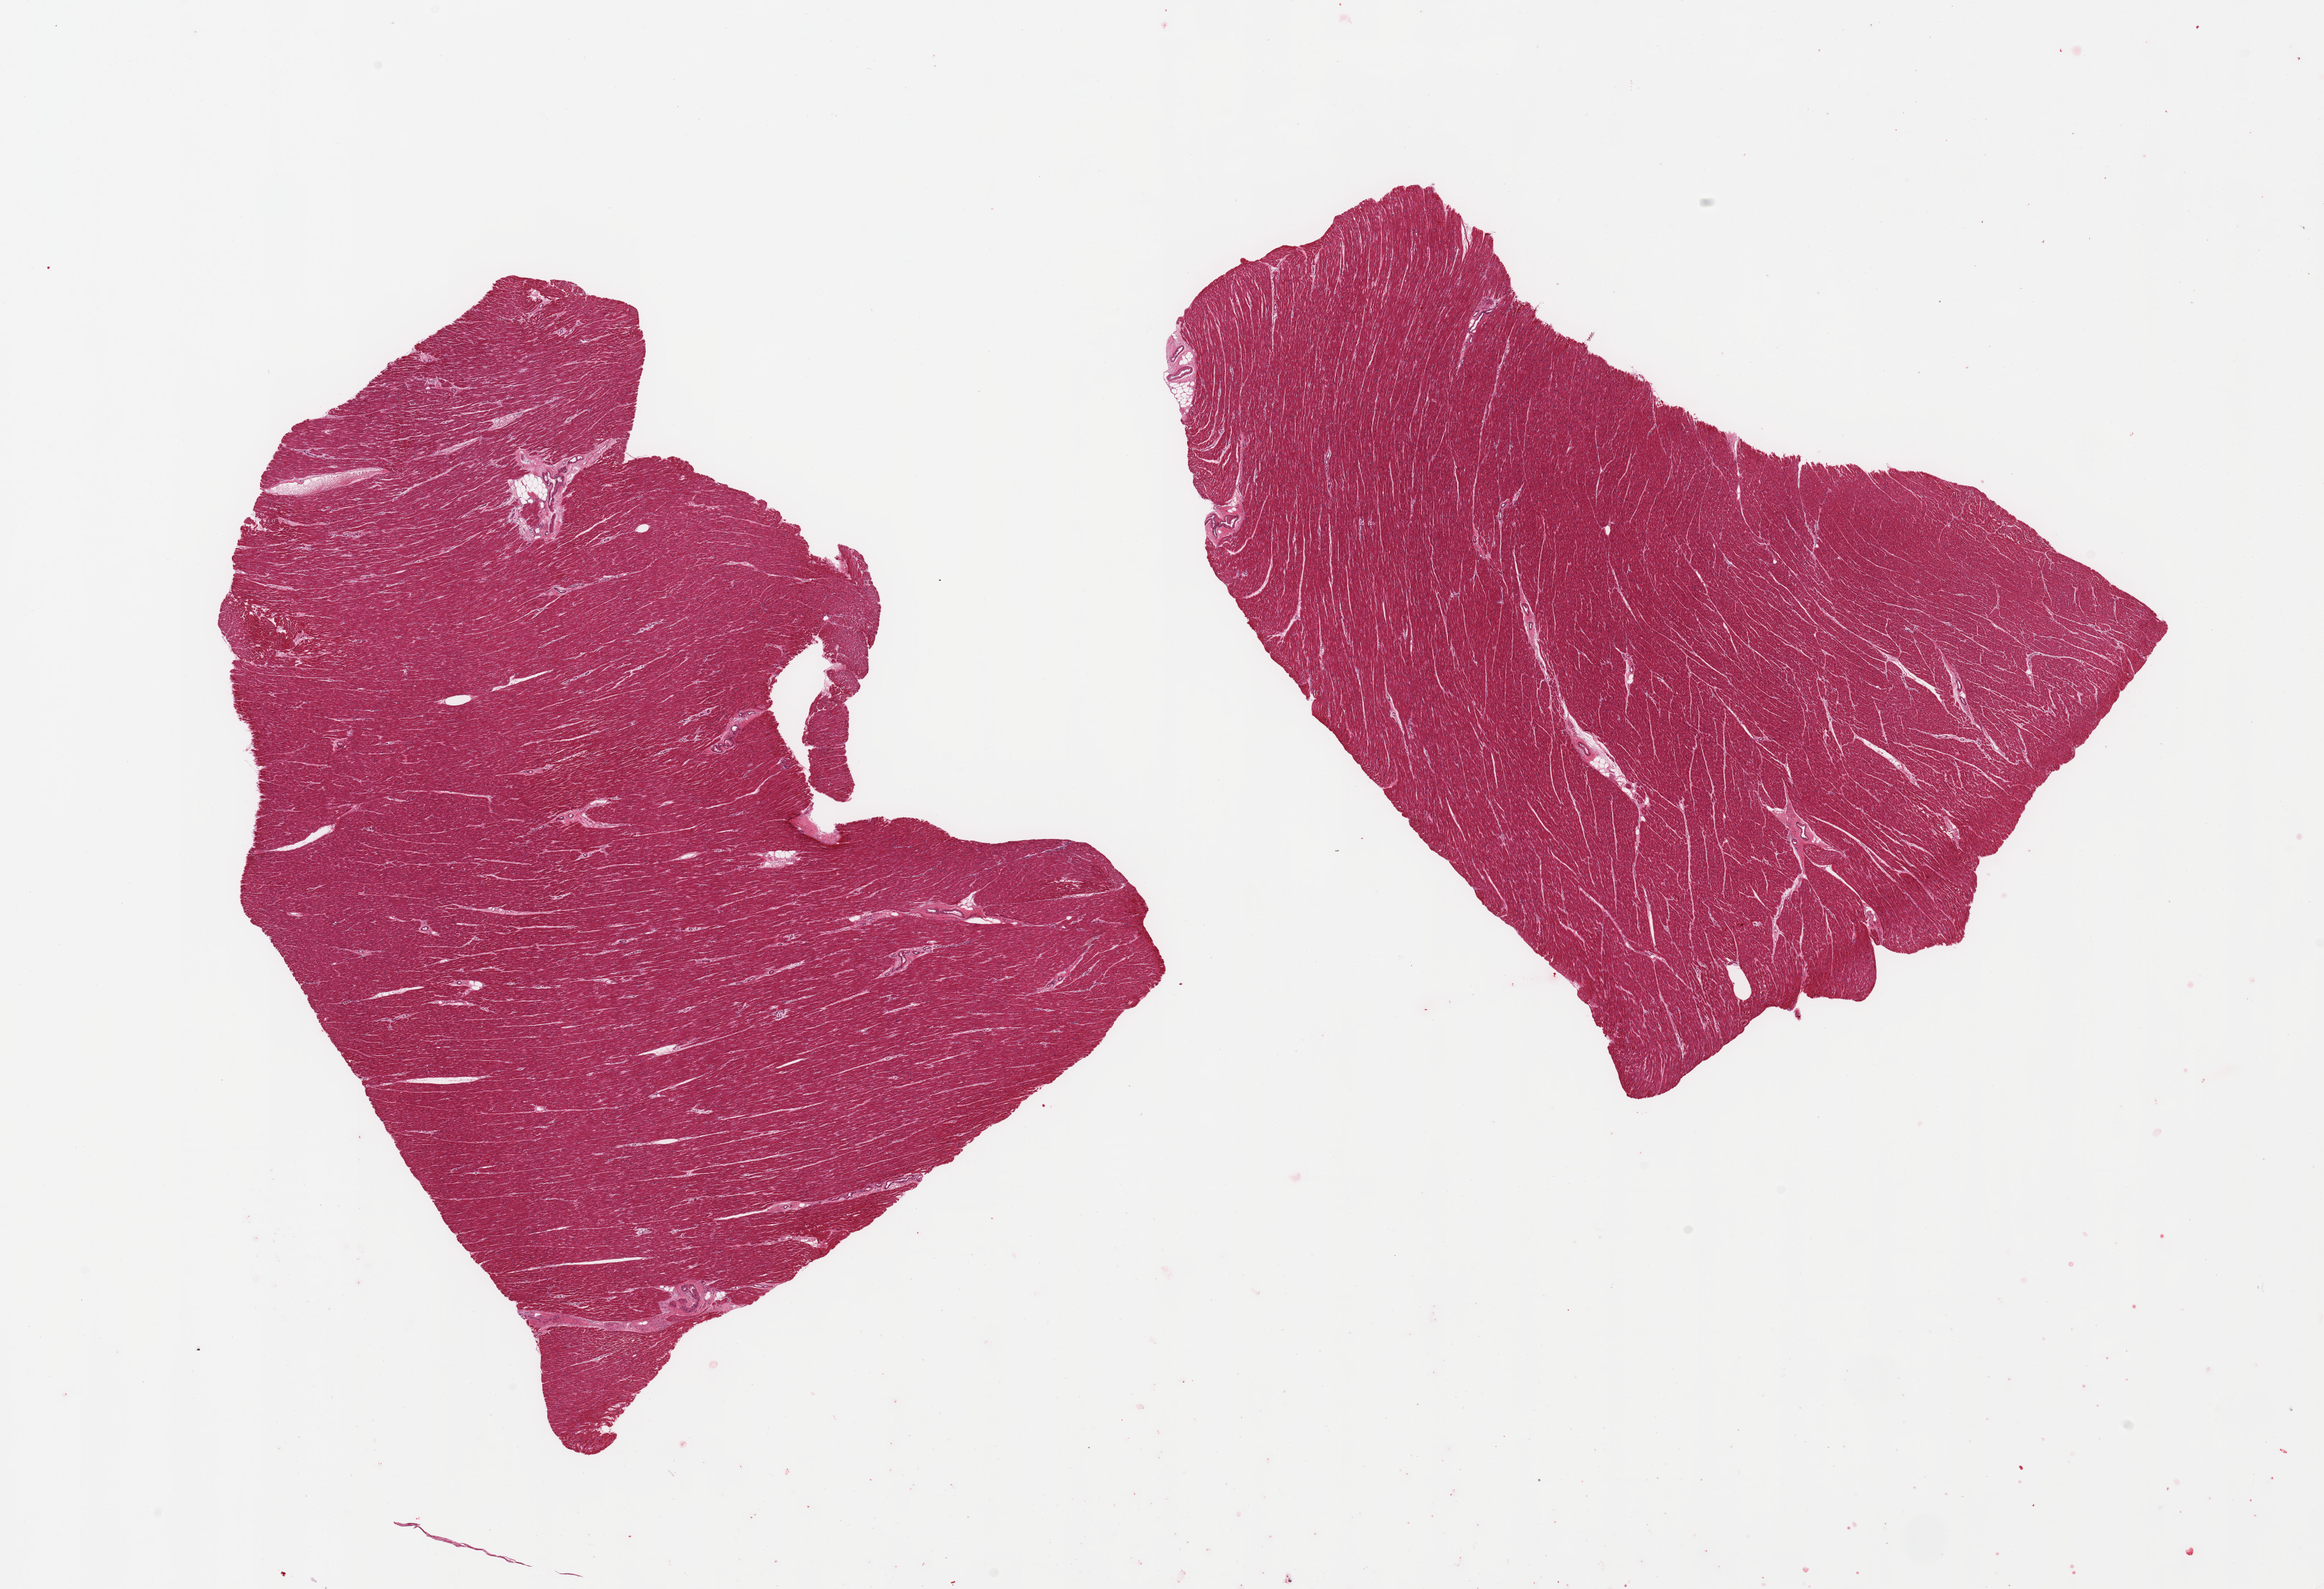
Whole-slide image, H&E stain — shown as a low-resolution overview of the whole scanned area (about 25.6 x 17.5 mm), PAXgene-fixed paraffin-embedded (PFPE) section, sampled site (target tissue): heart, donor tissue sample. Donor: male.
Reviewer comment on this tissue sample: 2 pieces, minimal chronic ischemic changes.